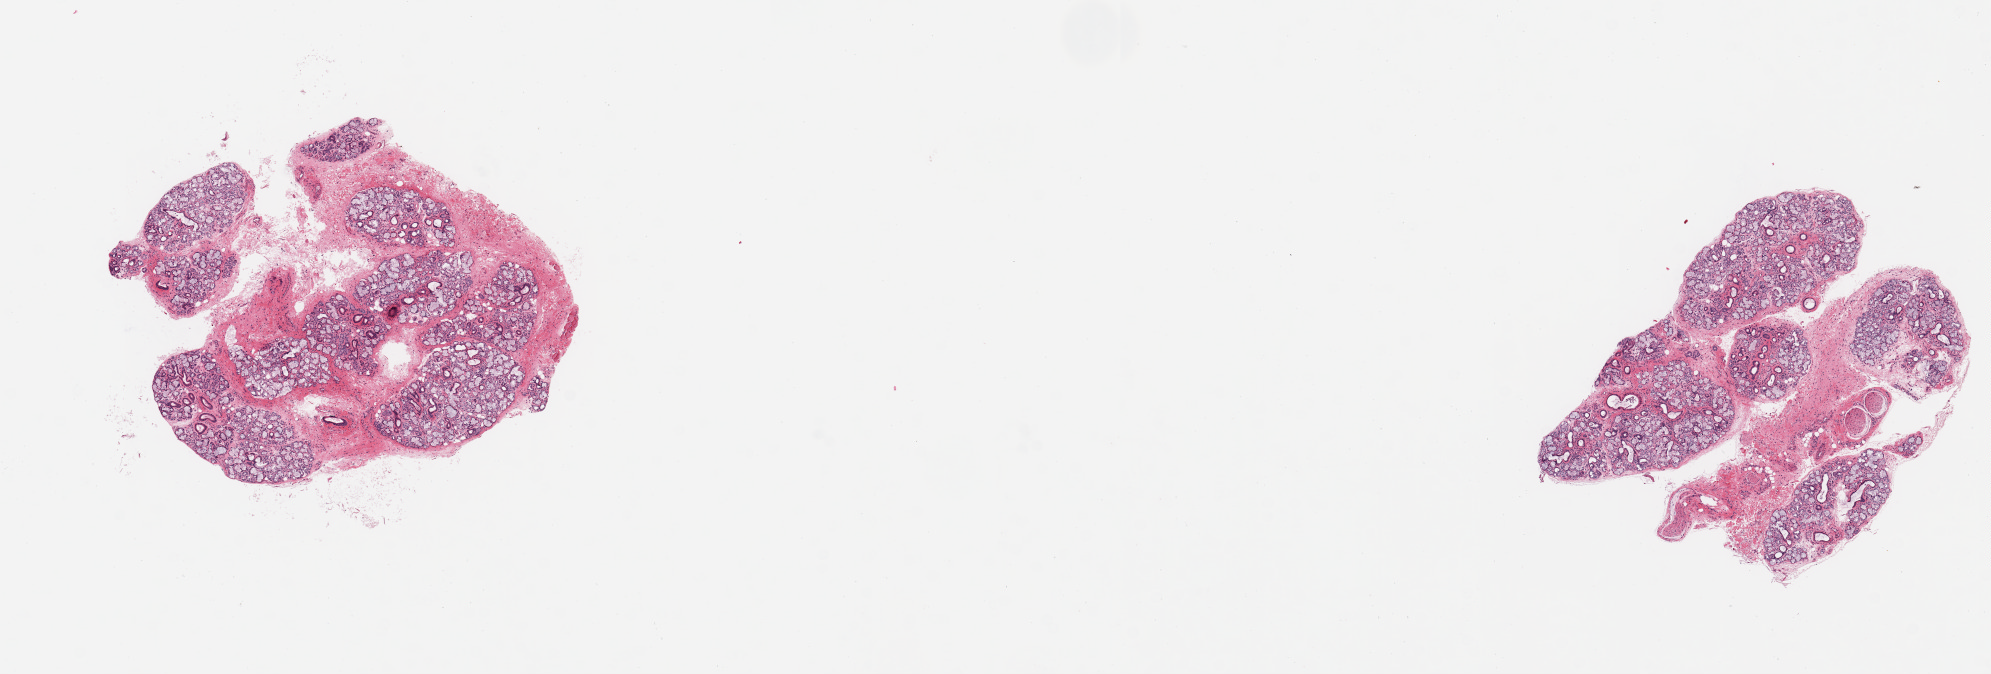
Digitized haematoxylin and eosin-stained section — low-resolution overview of the scanned area, about 15.8 x 5.3 mm (acquisition: 20x scan); PAXgene-fixed, paraffin-embedded tissue; target tissue: minor salivary gland; tissue donor sample. Donor sex: male.
Reviewer comment on this tissue sample: 2 pieces; well trimmed with 20% internal fibrous & neural content.